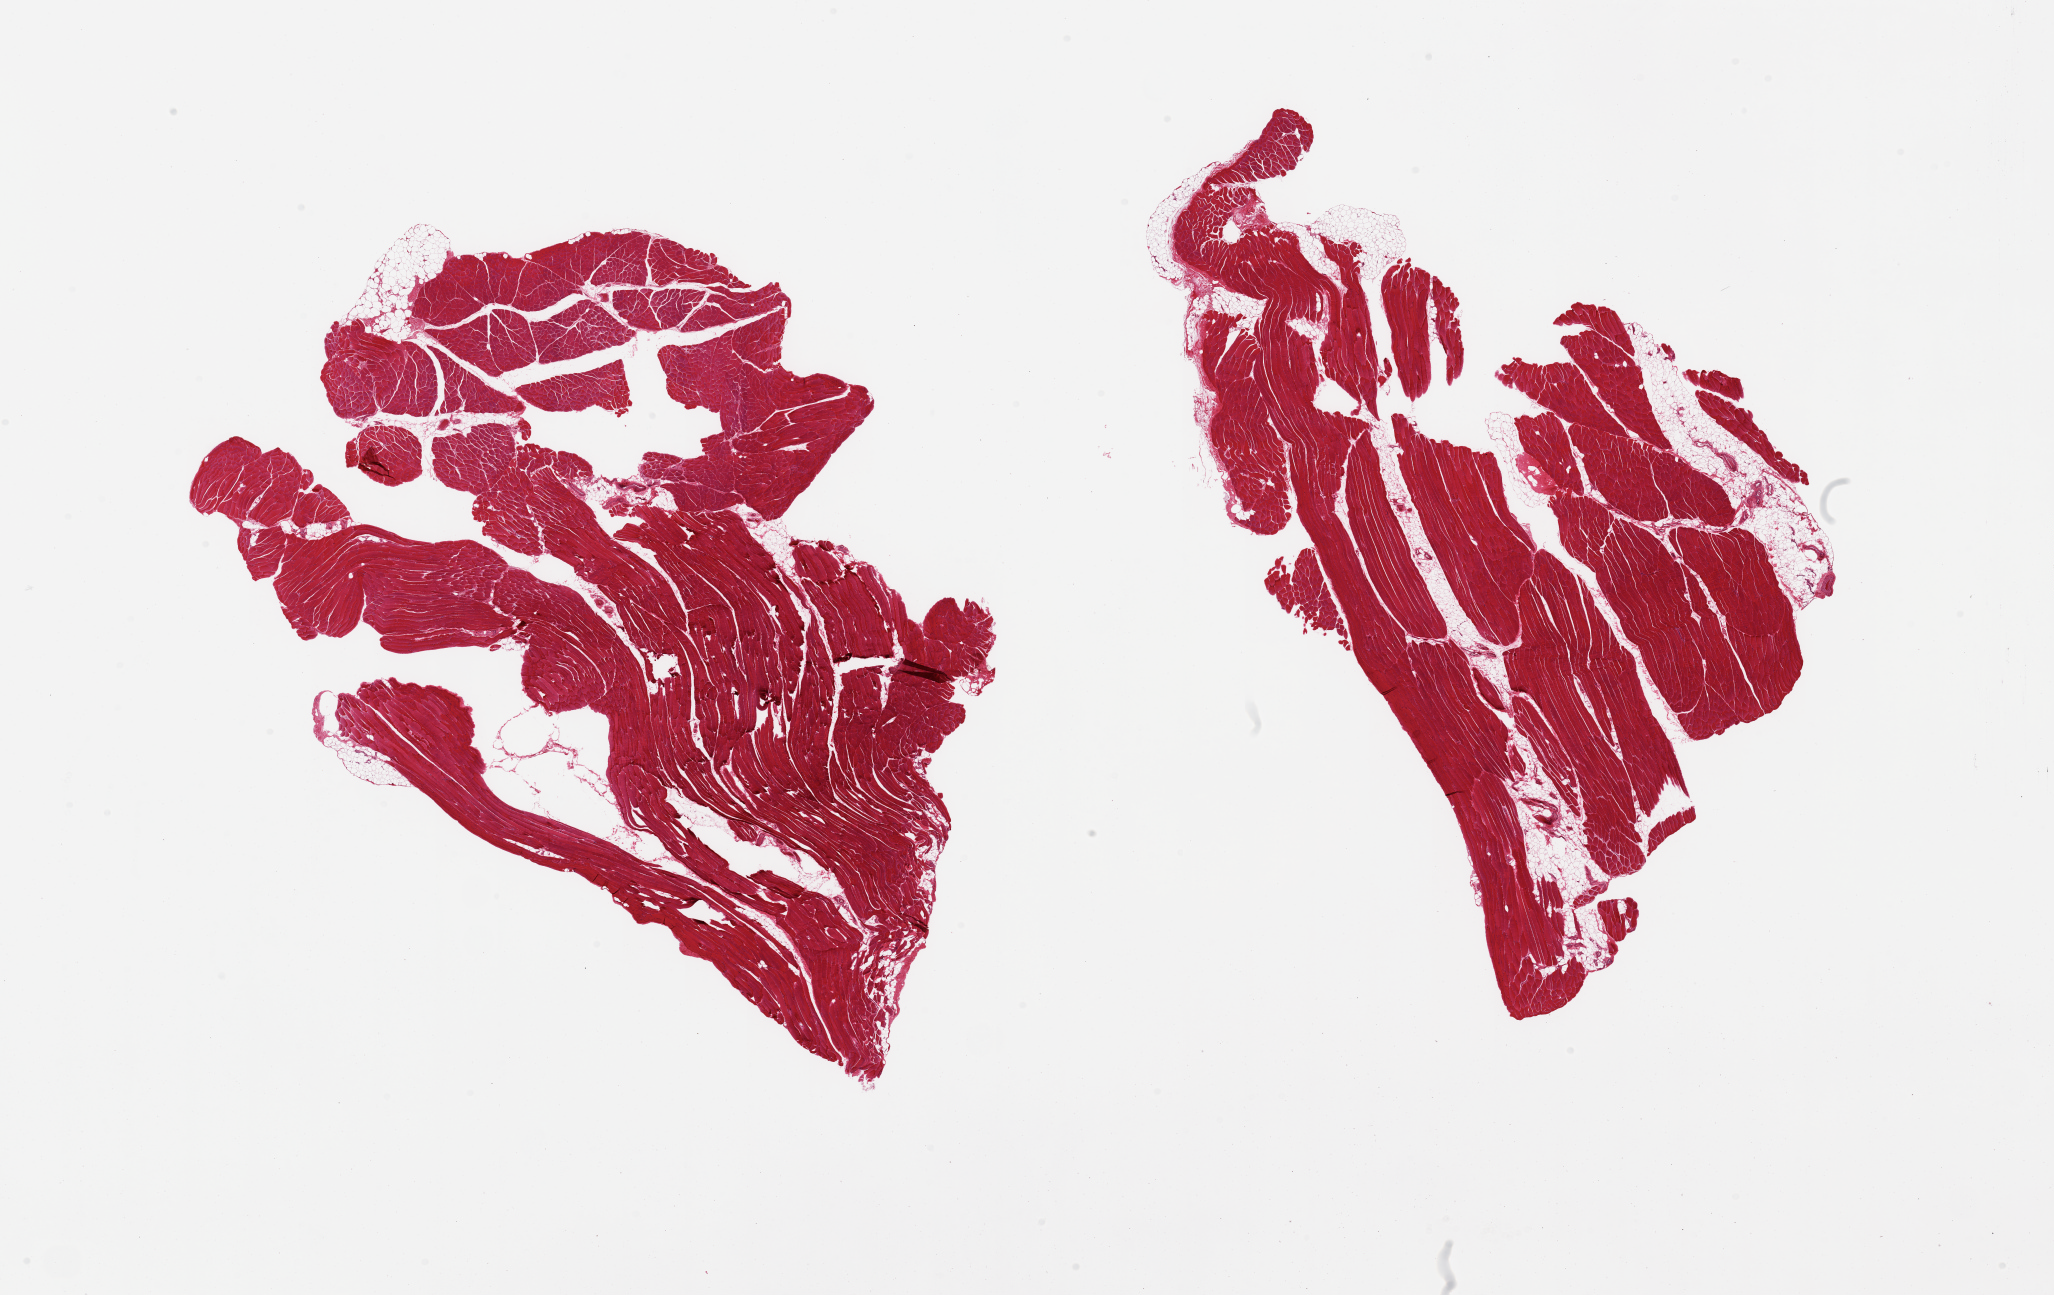
Whole-slide image, hematoxylin and eosin (H&E) stain — shown as a low-resolution overview of the whole scanned area (about 32.5 x 20.5 mm). PAXgene-fixed, paraffin-embedded tissue. Section of skeletal muscle (target tissue). Donor tissue sample. Donor sex: female.
Pathologist's review note for this sample: 2 pieces. 10% internal fat.